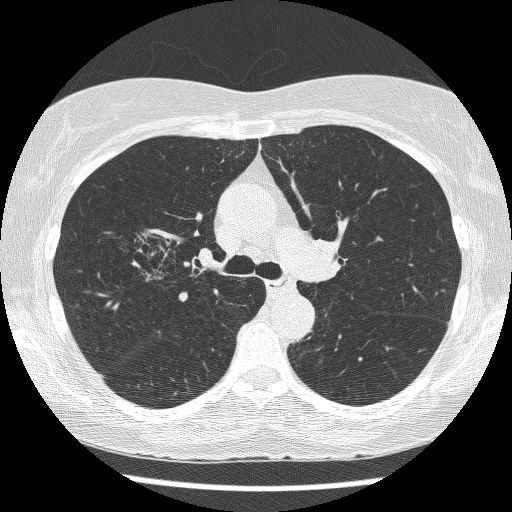
Low-dose screening chest CT, axial slice. Baseline annual screen. Lung window (W 1500 / L -600 HU). 1.25 mm slice thickness. Slice 181 of 271 in the series. 512 × 512 image matrix. Female, age 64 years at enrolment.
Lesion marked by an expert reader, bounding box [x1, y1, x2, y2] px = [126, 225, 206, 300]. The screening reader recorded 3 non-calcified nodules or masses ≥4 mm on this exam (right upper lobe, right upper lobe, left lower lobe); which of them this box marks is not recorded. Official screen result: positive, change unspecified: nodule(s) >= 4 mm or enlarging nodule(s), mass(es), or other non-specific abnormalities suspicious for lung cancer. Lung cancer was diagnosed 735 days after this screen: adenocarcinoma, NOS, right upper lobe, right middle lobe, right hilum, stage IV (AJCC 6th edition), 85 mm at pathology.